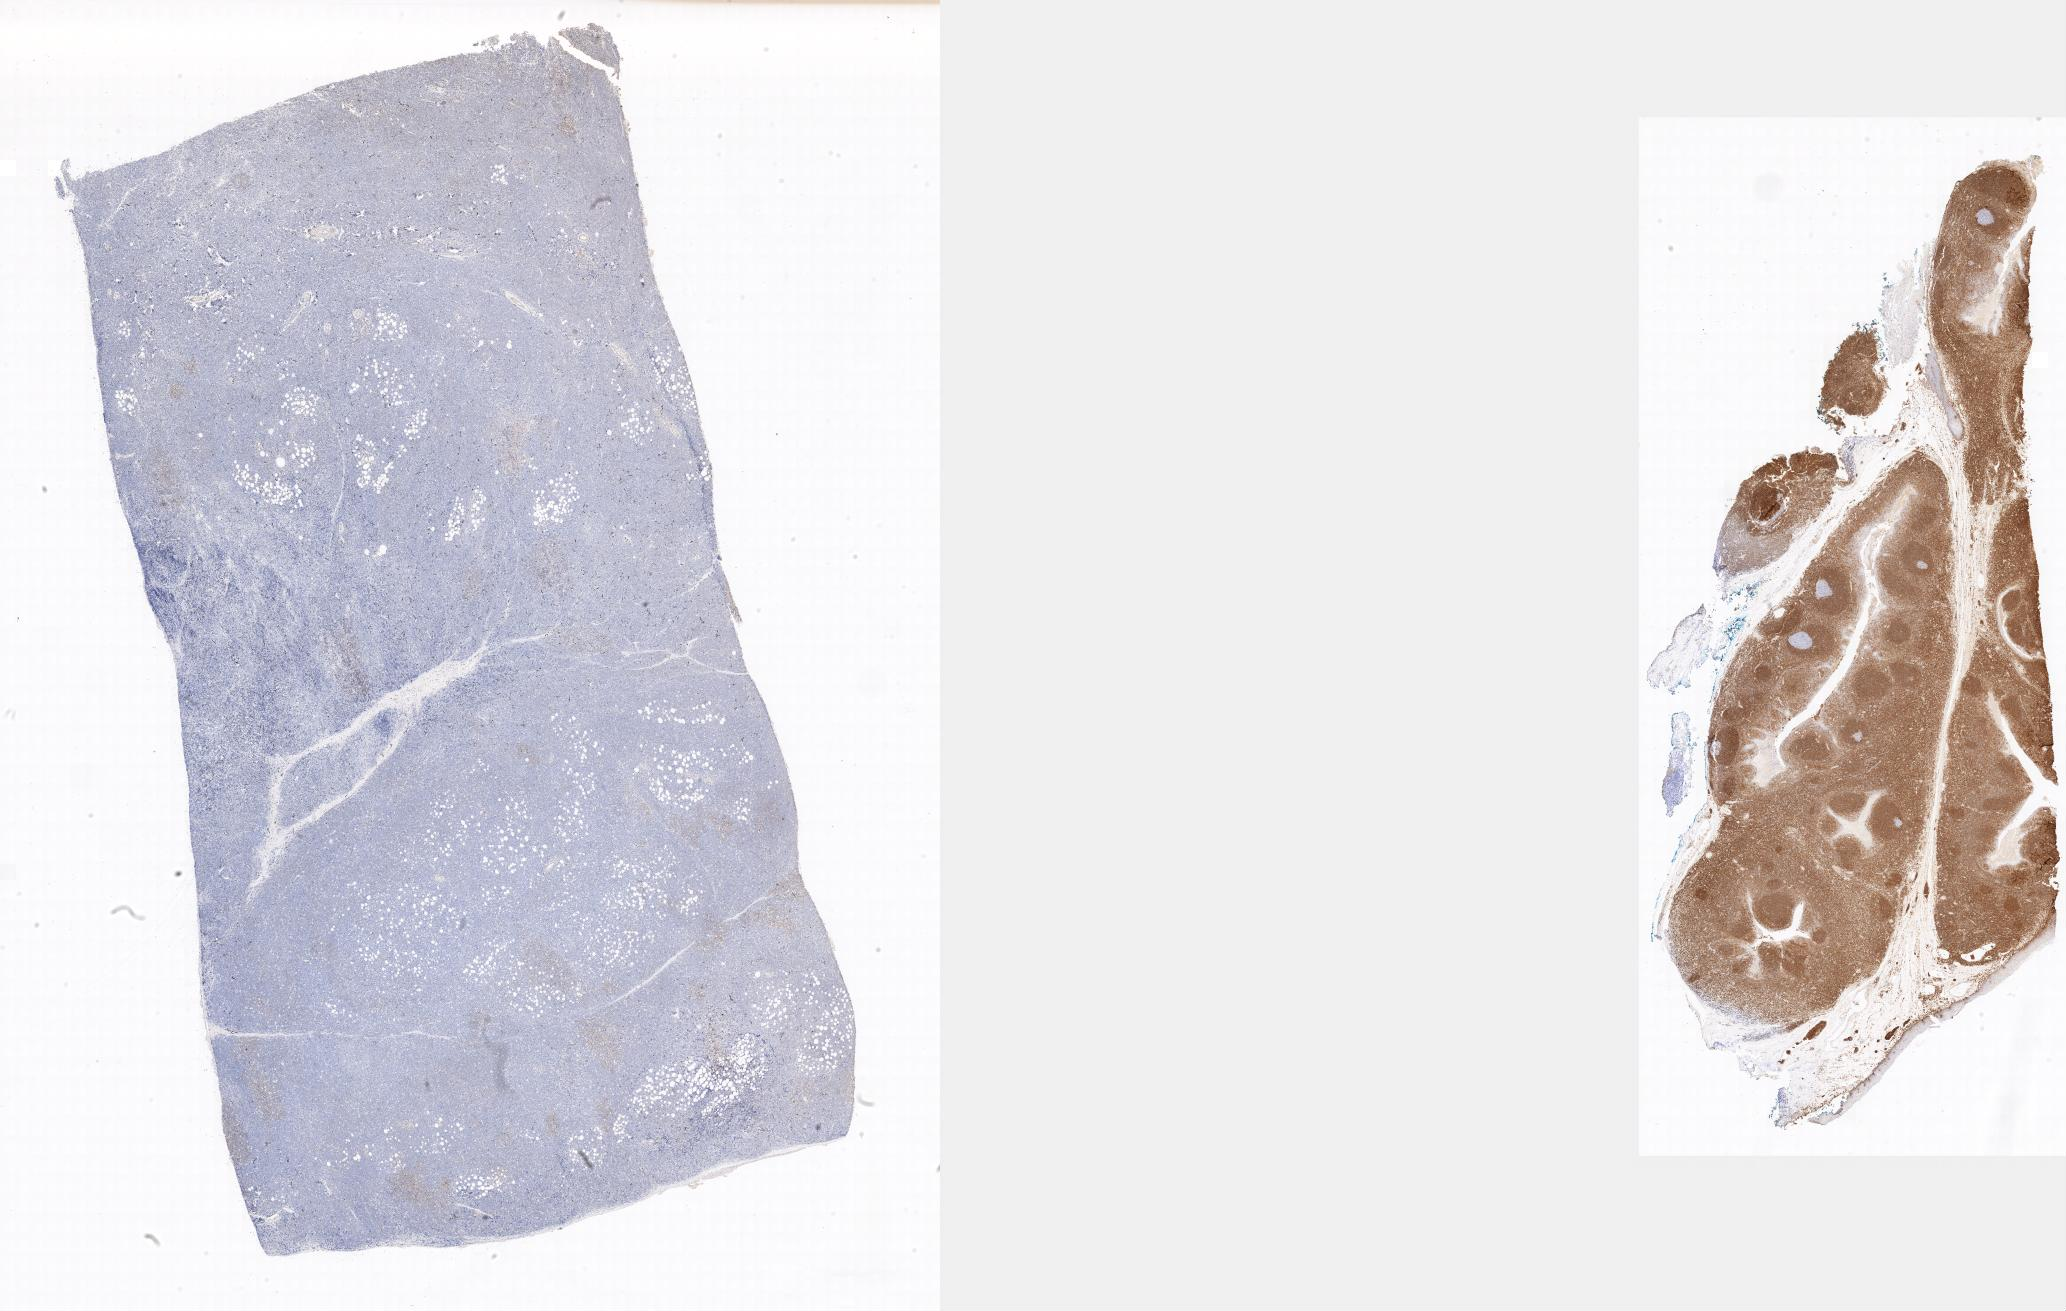
IHC for BCL2, whole-slide image, shown as a low-resolution overview of the whole scanned area. Tumor tissue. Site: colon. Patient: female, aged 12.
Histologic diagnosis: Burkitt lymphoma, NOS.